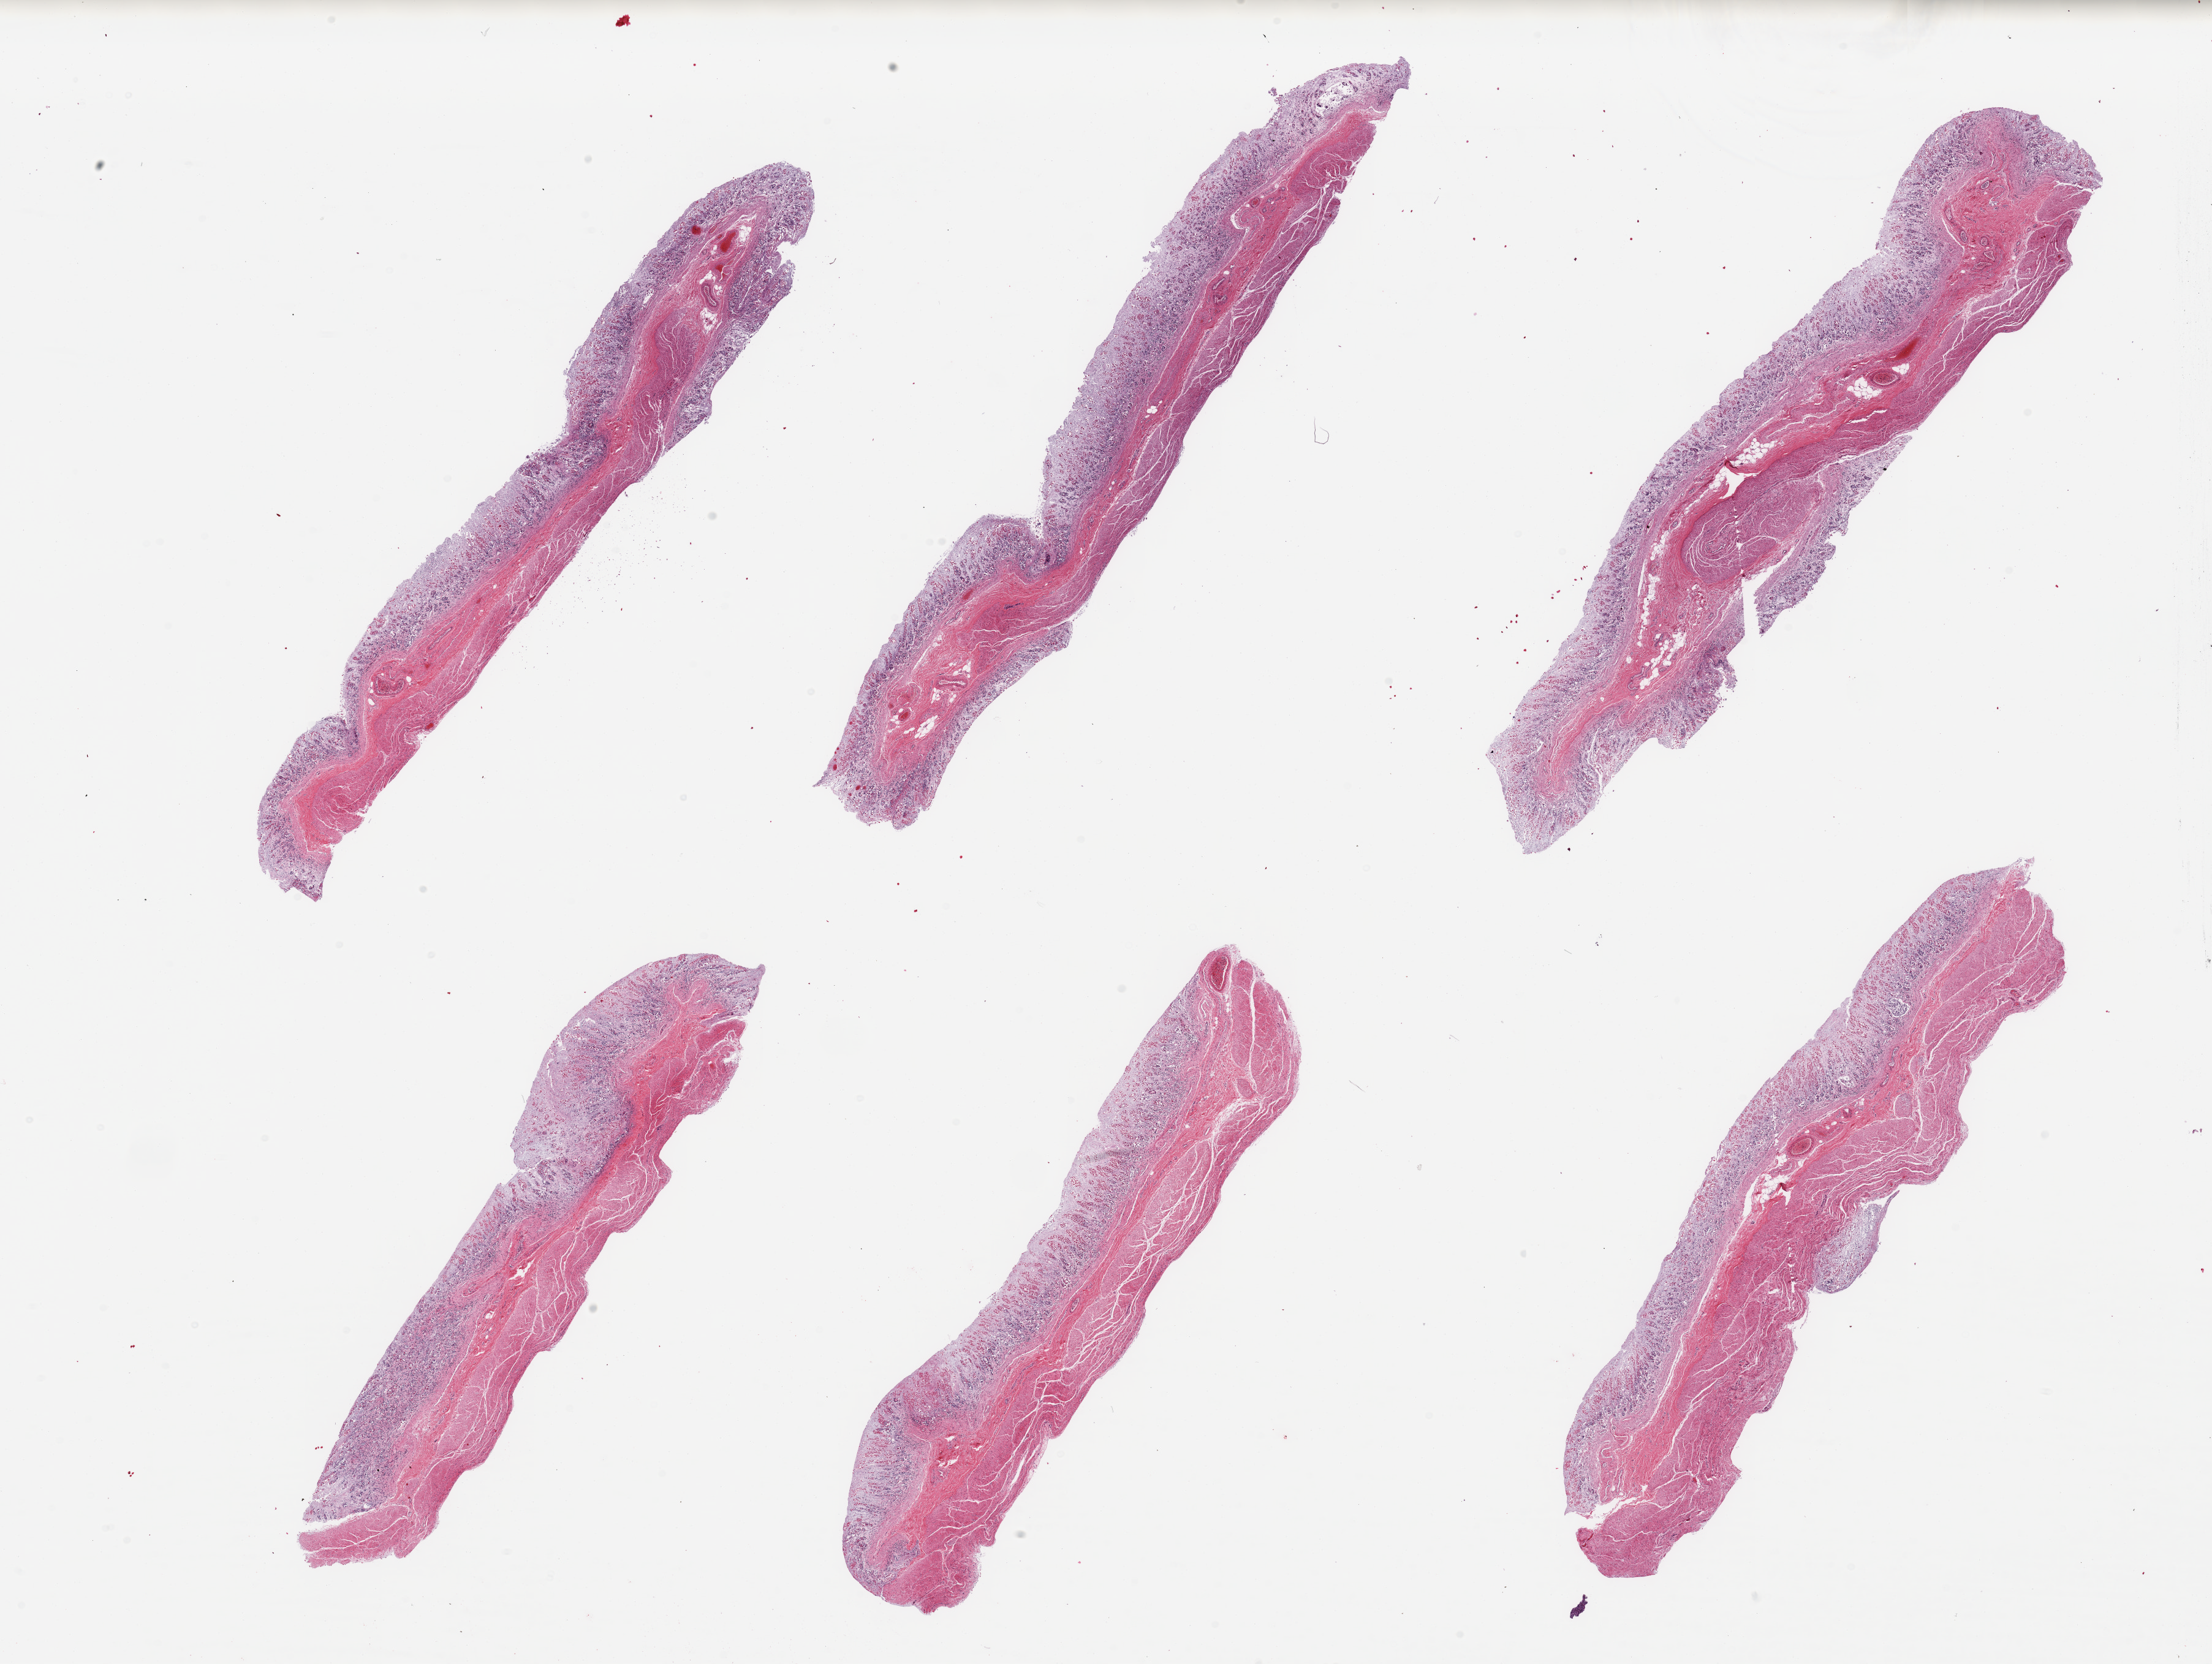
Haematoxylin and eosin whole-slide image, brightfield, whole scanned area (about 28.5 x 21.5 mm) shown as a low-resolution overview; PAXgene-fixed, paraffin-embedded tissue; sampled site (target tissue): stomach; donor tissue sample. Donor sex: female.
Pathologist's review note for this sample: 6 pieces; mucosa severely autolyzed; muscularis moderately autolyzed.